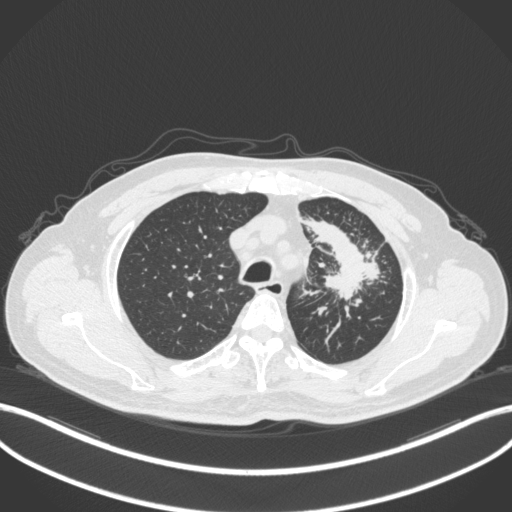
Chest CT, one axial slice. Reconstruction kernel B31f. 120 kVp. Lung window (W 1500 / L -600 HU). 512 × 512 image matrix, field of view 400 × 400 mm. Patient: male, 69 years. From the clinical record (not read from this slice): clinical TNM (as recorded): T2a N2 M0; histopathological grade: G2-3.
Outlined on this slice (bounding box drawn by a radiologist):
- lung tumour (recorded histology: adenocarcinoma): bounding box (x1, y1, x2, y2) in pixels: (296, 212, 384, 307)